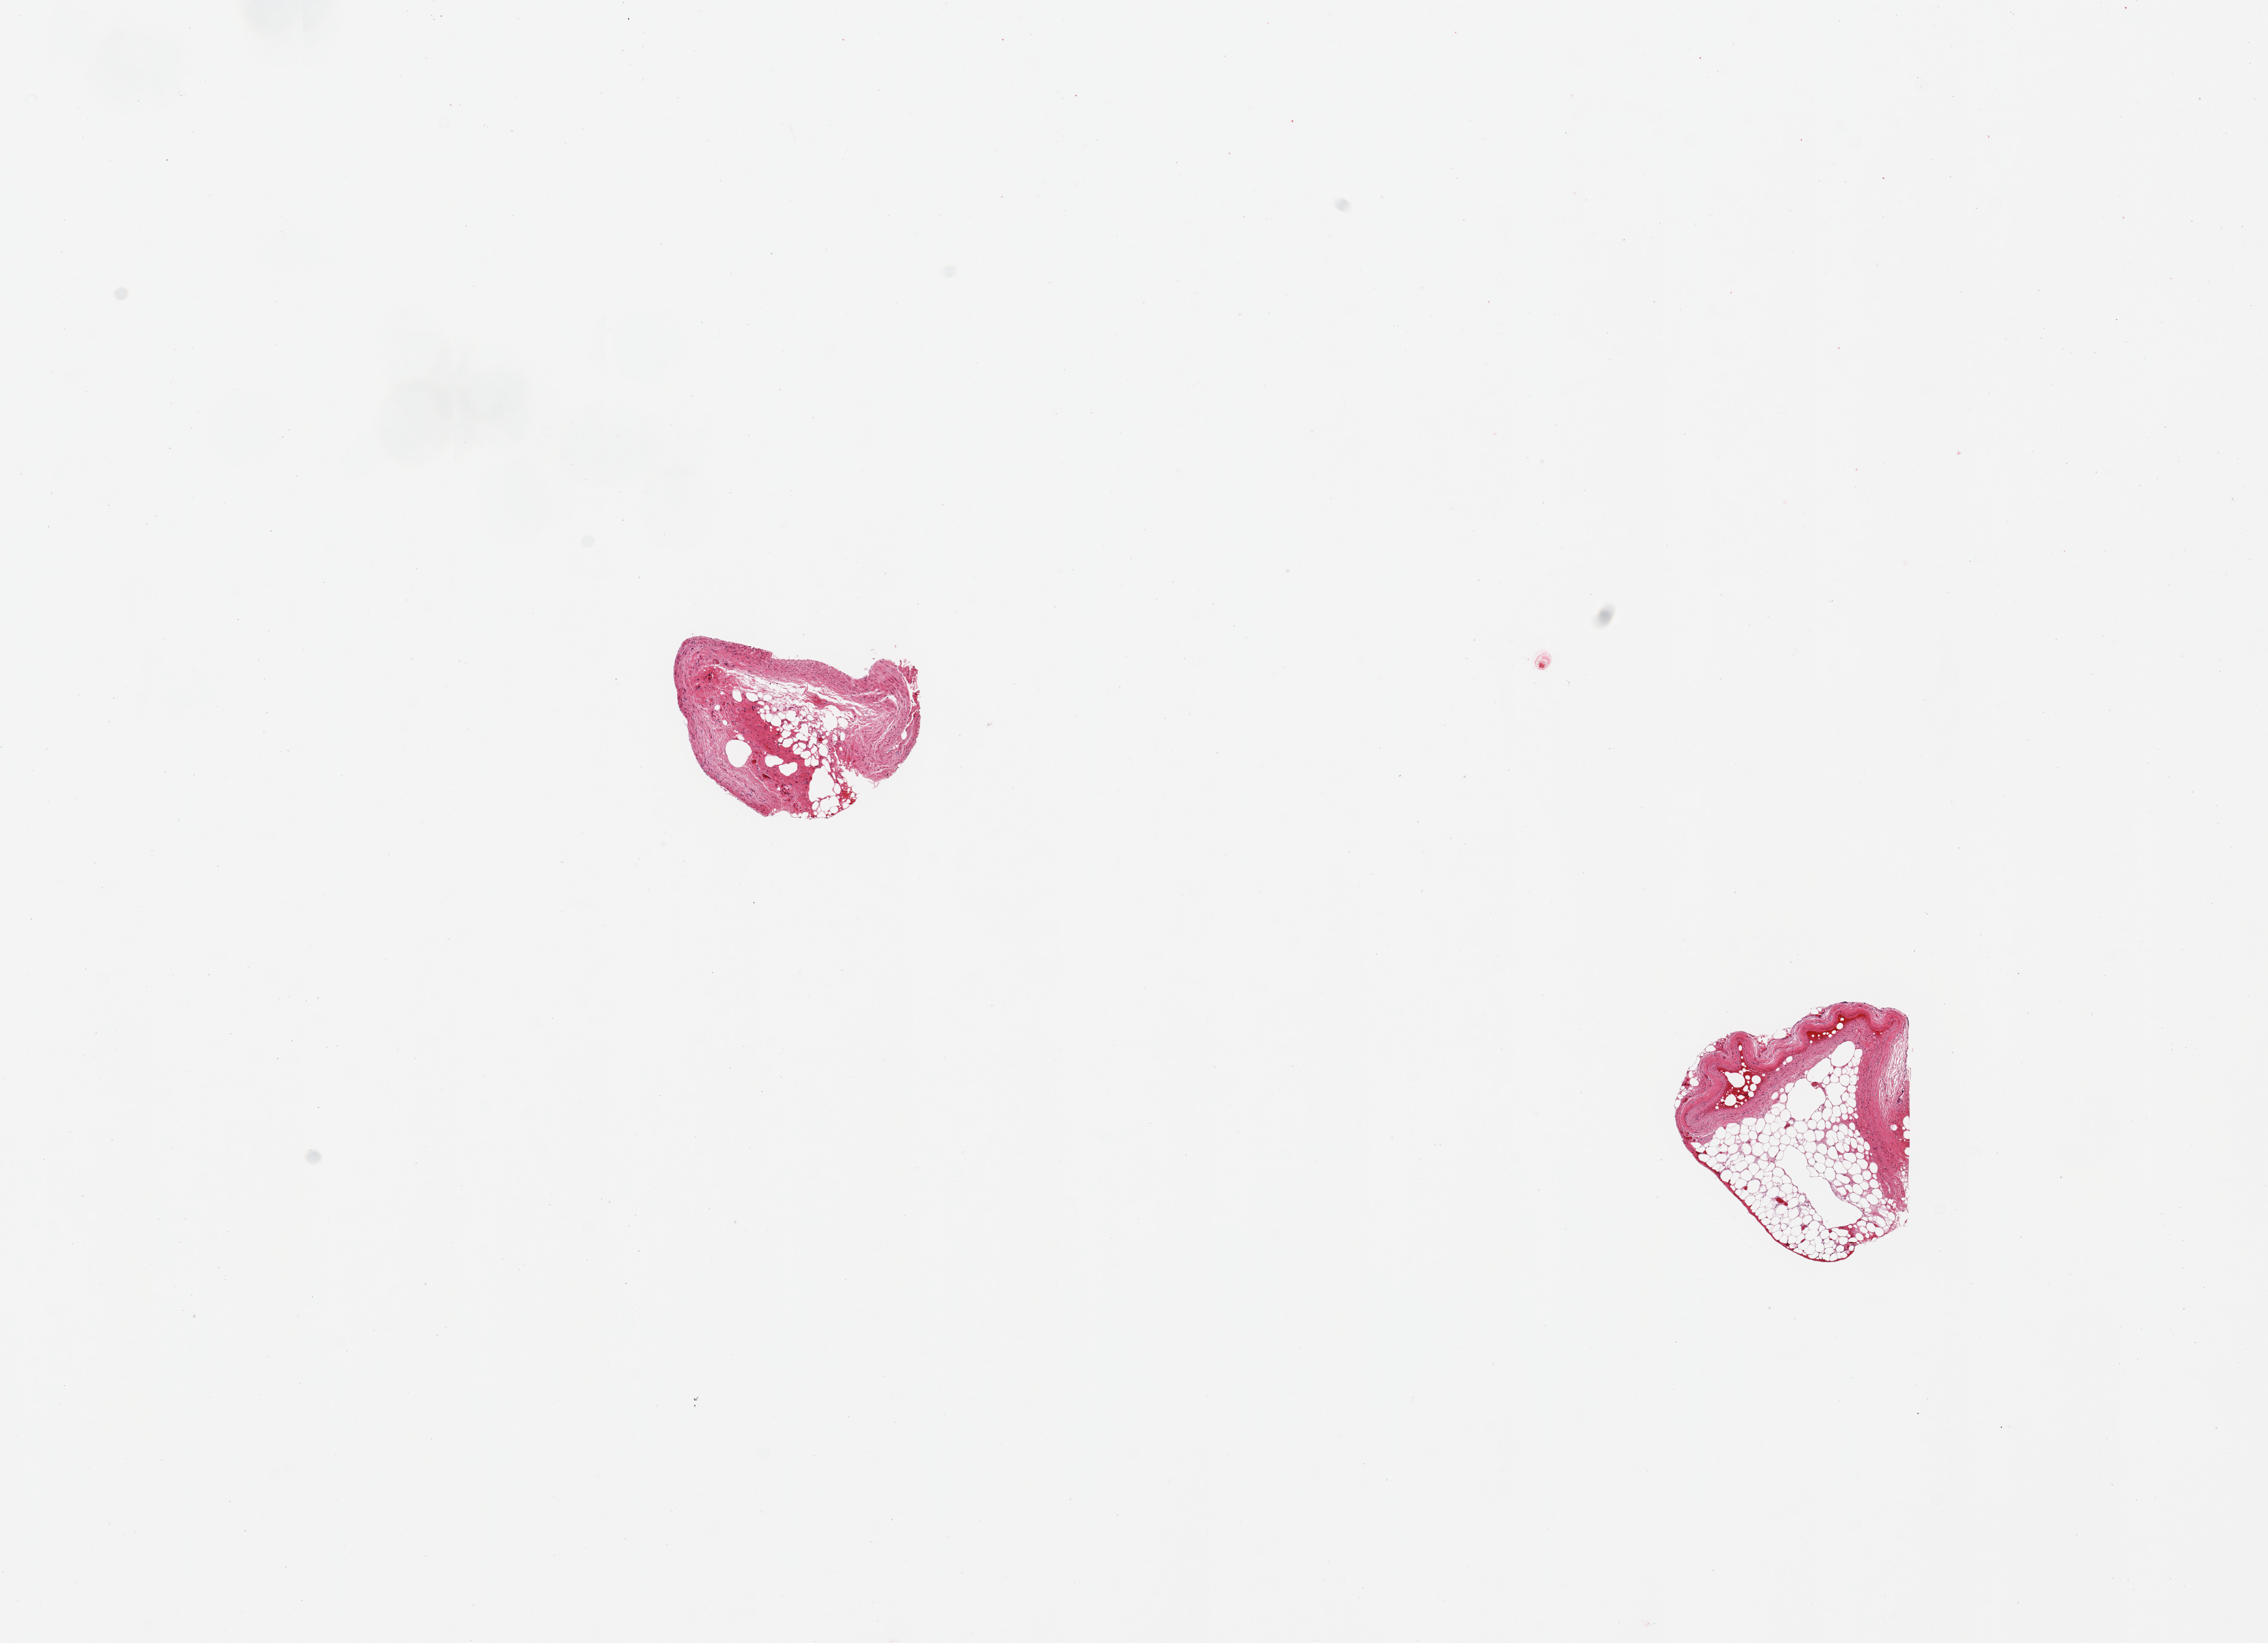
Whole-slide image, haematoxylin and eosin stain — whole scanned area (about 14.8 x 10.7 mm) shown as a low-resolution overview; PAXgene-fixed, paraffin-embedded tissue; target tissue: coronary artery; tissue donor sample. Female donor.
Reviewer comment on this tissue sample: 2 pieces; 60% external fat.